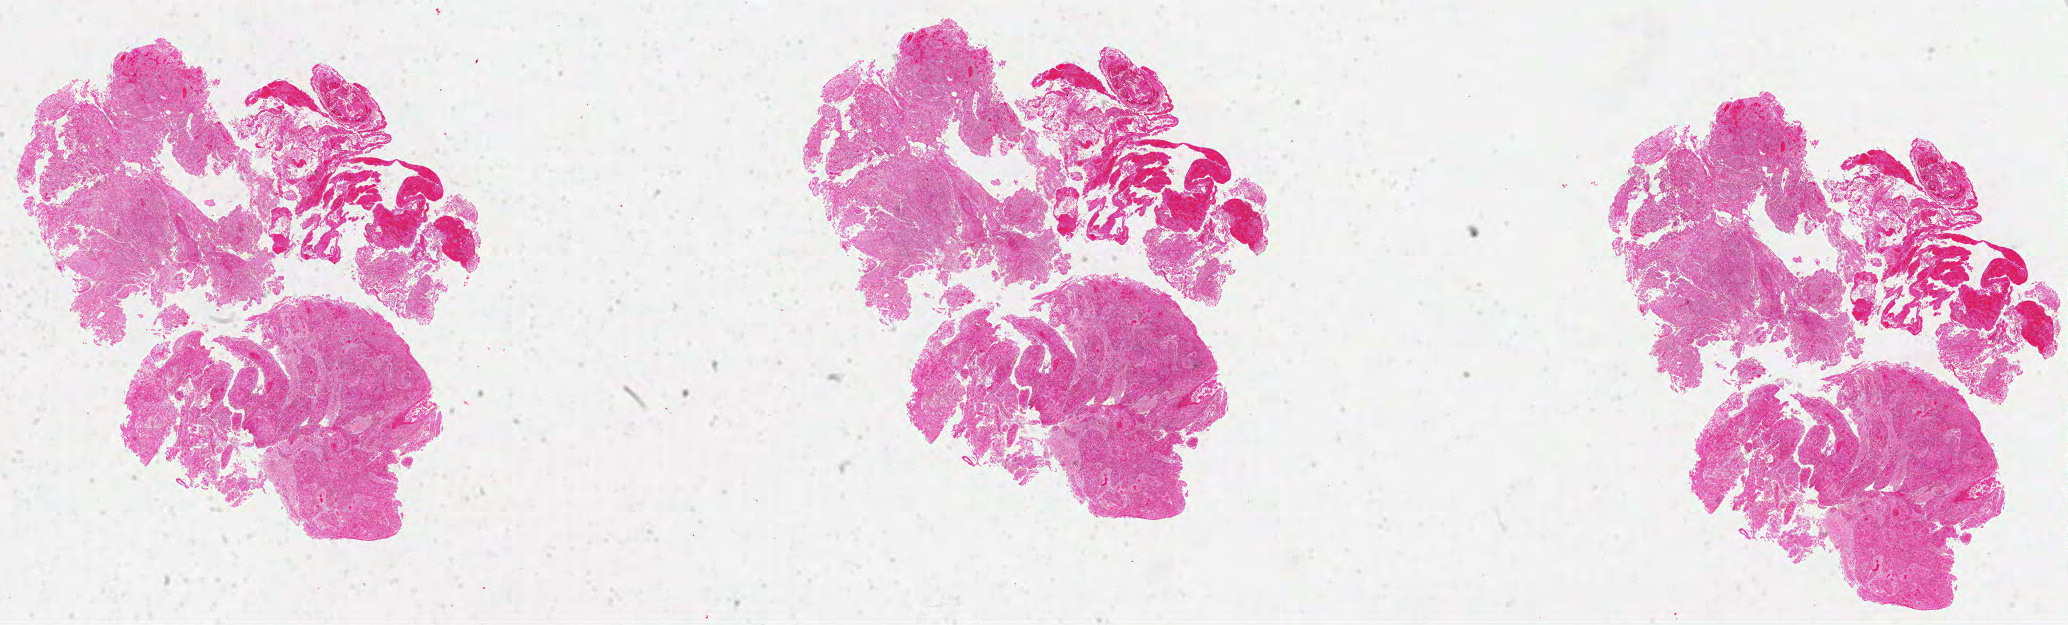
Whole-slide histology image, H&E — a low-resolution overview of the entire scanned area, about 33.4 x 10.1 mm (from a 40x scan). Formalin-fixed paraffin-embedded (FFPE) diagnostic section. Primary tumour sample from the head and neck. Male patient; age at initial diagnosis 47 years. Histologic grade: G2 (moderately differentiated).
* histologic diagnosis: Squamous cell carcinoma, NOS